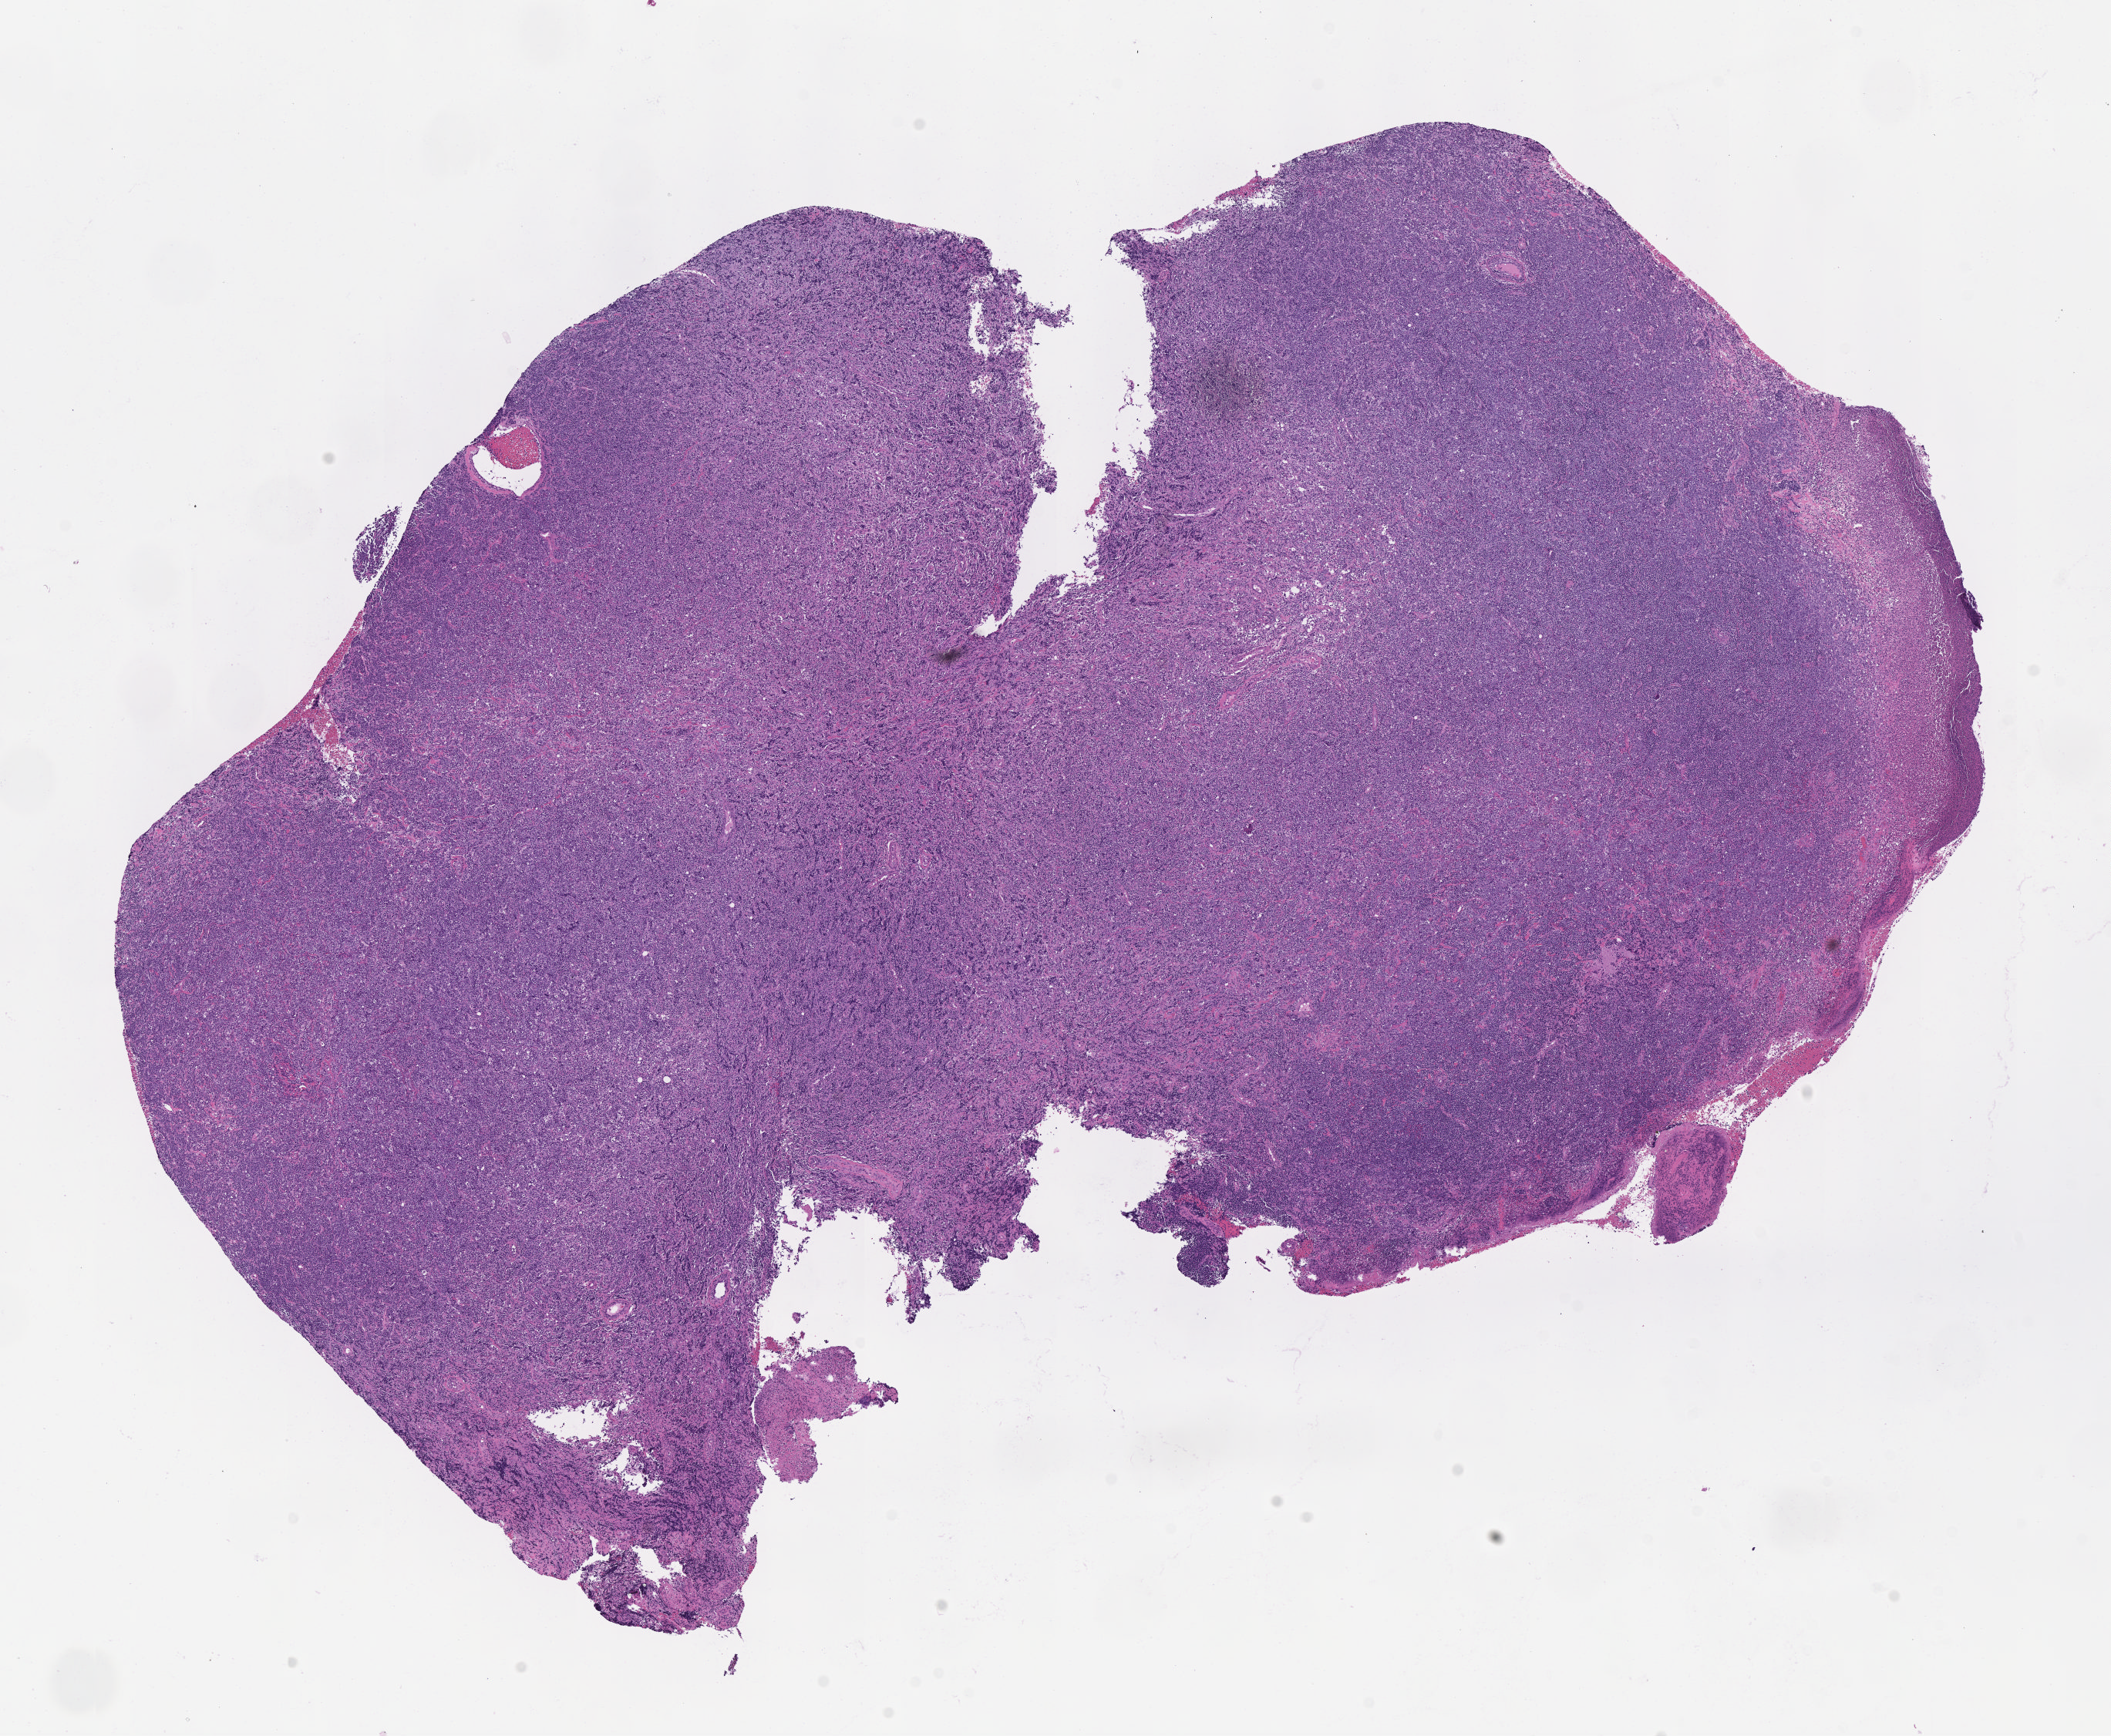
Whole-slide image, H&E stain — a low-resolution overview of the entire scanned area, about 11.1 x 9.1 mm, specimen: tumor tissue. Male, age 7 years at initial diagnosis.
Histologic diagnosis: Diffuse large B-cell lymphoma, NOS.